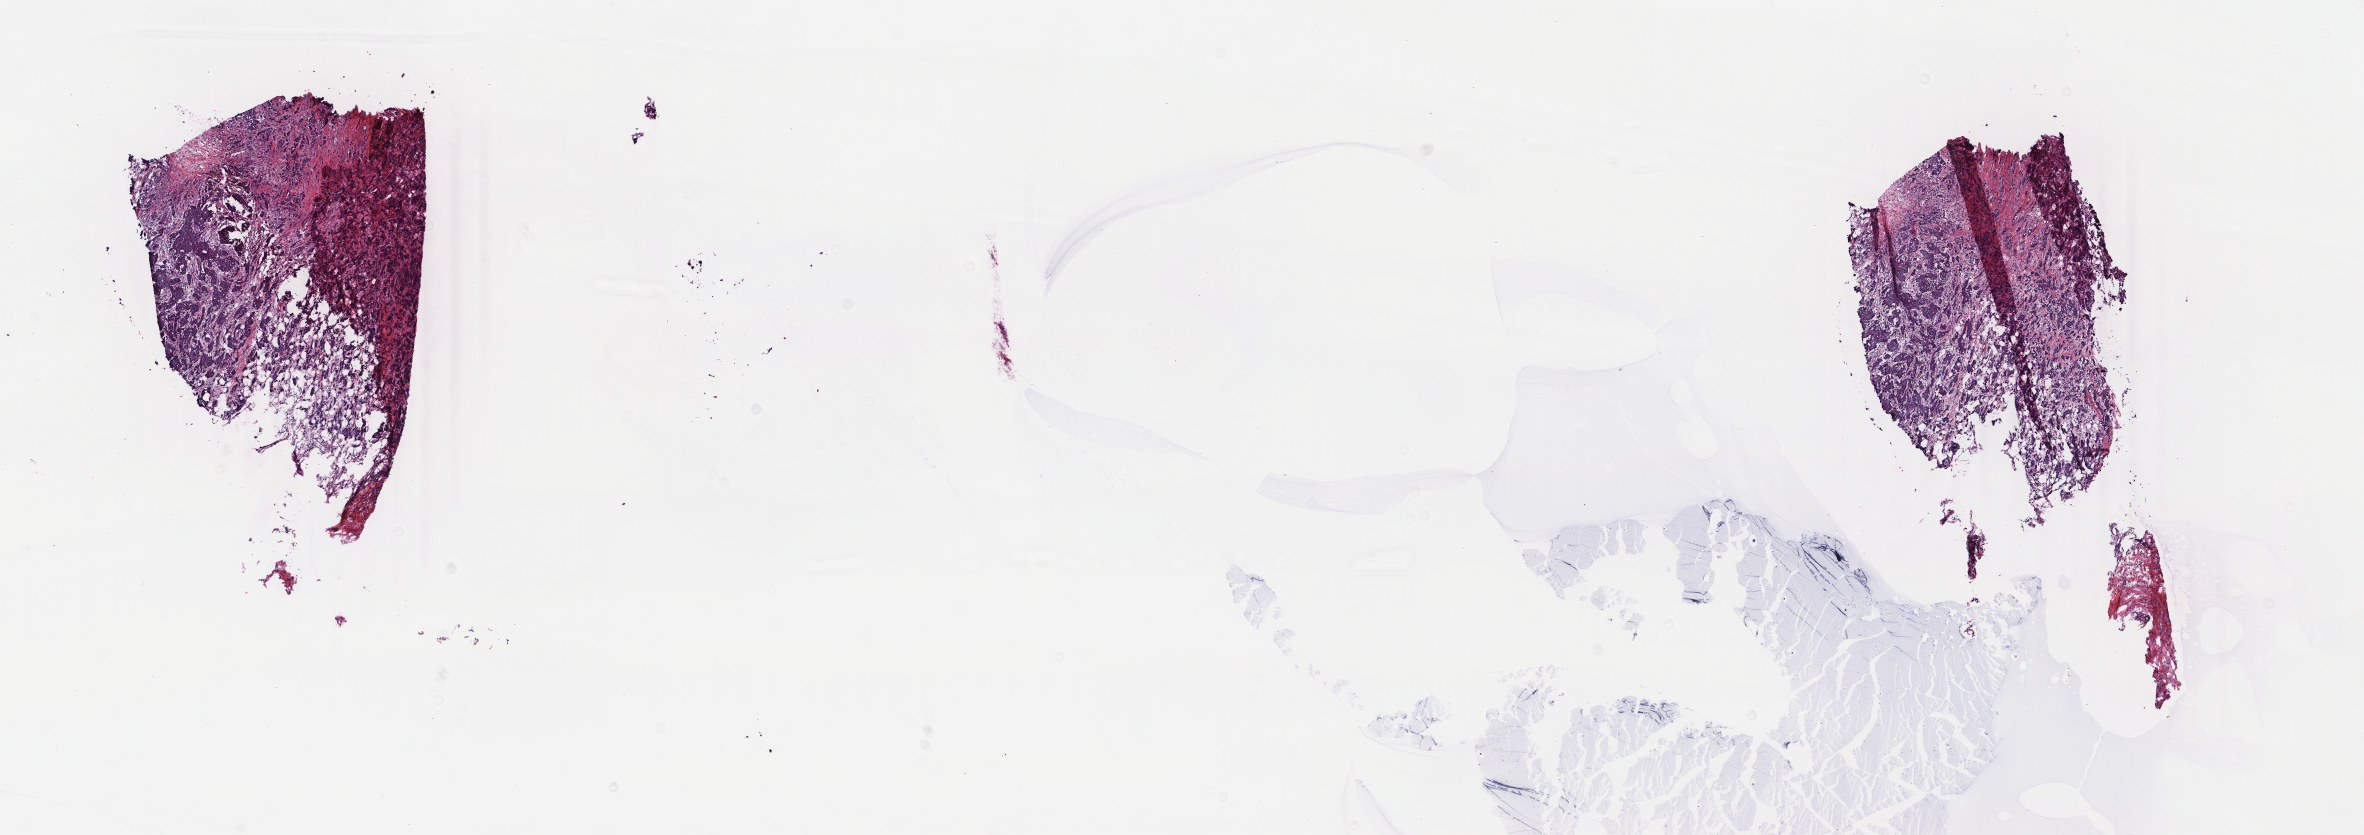
H&E-stained whole-slide image — whole scanned area (about 18.8 x 6.6 mm, acquisition: 40x scan) shown as a low-resolution overview, frozen section from the bottom of the tissue portion, sample: primary tumour, breast. Female patient; age at initial diagnosis 44 years.
Diagnosis: Infiltrating duct carcinoma, NOS.